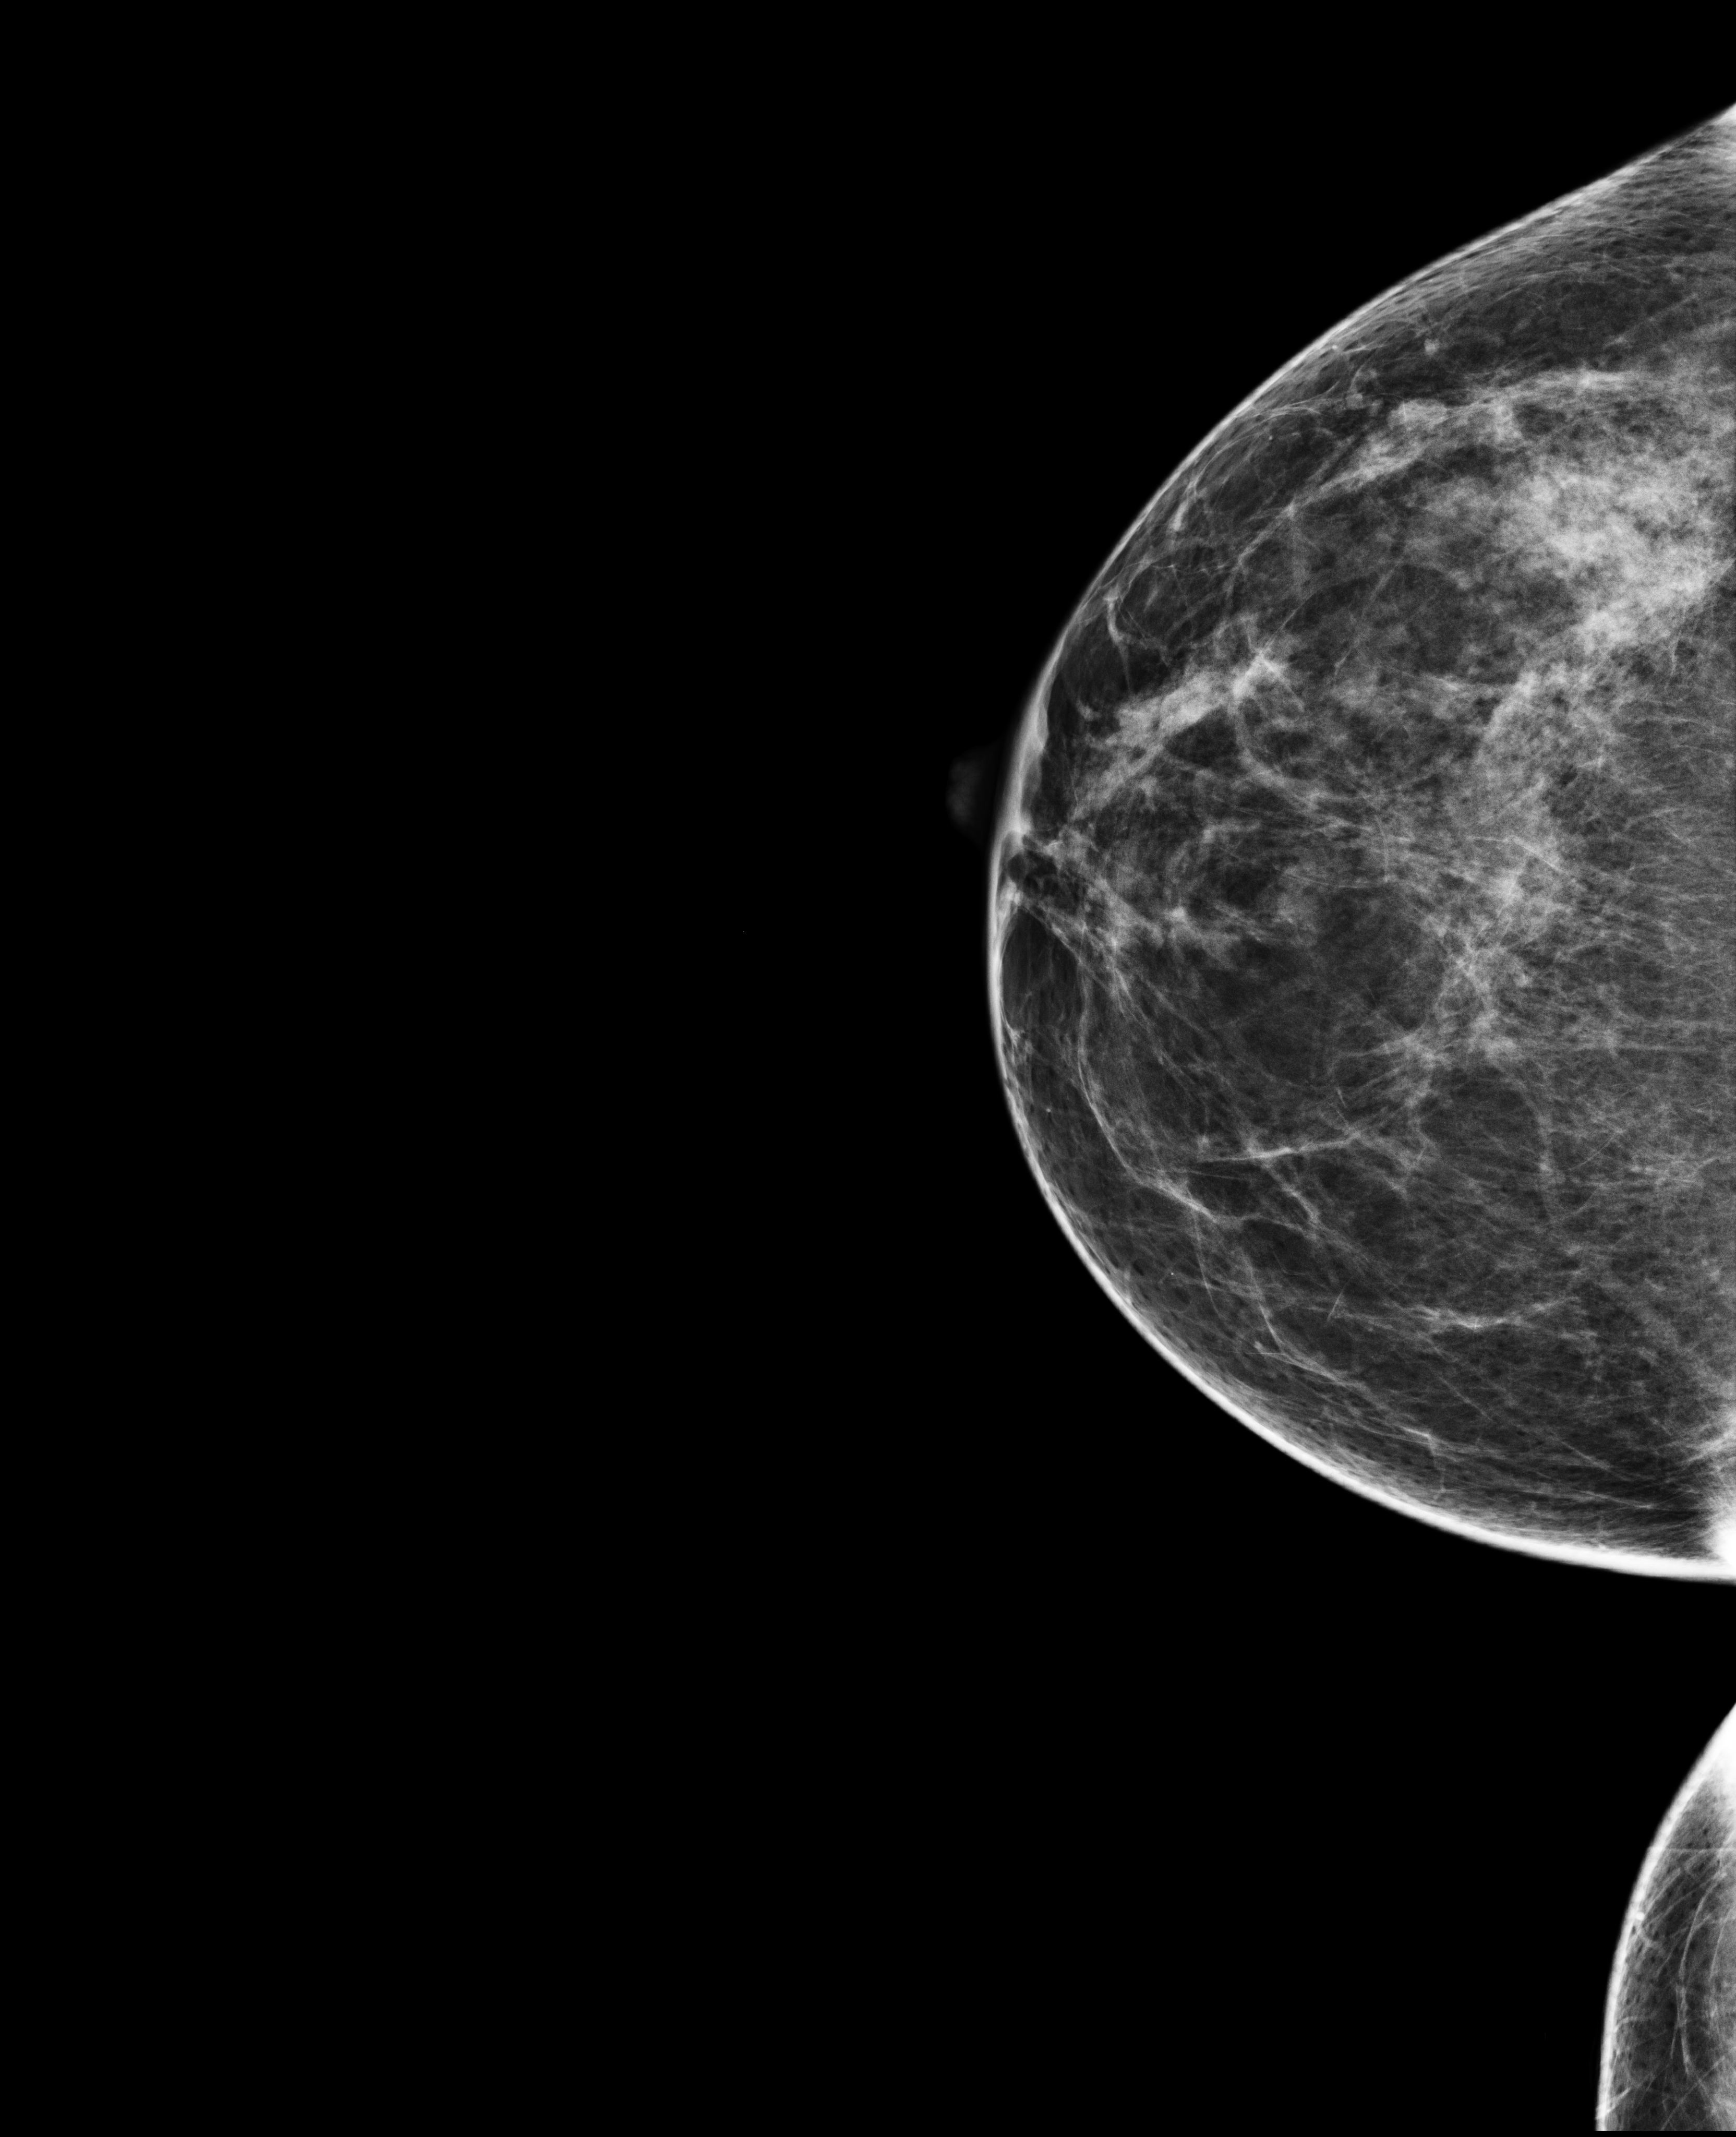
Annual screening mammography examination. Patient aged 52 years (female).
Image type: full-field digital mammogram. Breast: right. Projection: cranio-caudal projection.